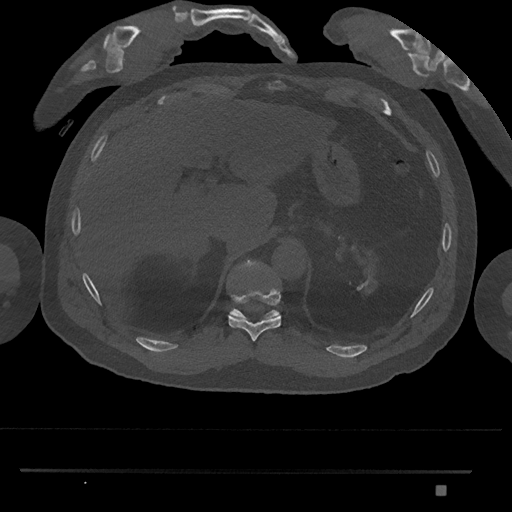
CT including the spine, one axial slice. Position 987 of 1134 along the scan axis. 120 kVp. Bone window (W 1800 / L 400 HU). 512 × 512 image matrix, field of view 429 × 429 mm. Male patient, age 65 years. Case-level facts recorded for this patient, not image findings: primary cancer: prostate.
Outlined on this slice (semi-automatic segmentation, software-assisted and operator-edited):
- T10 vertebra: bounding box (x1, y1, x2, y2) in pixels: (228, 288, 281, 341)
- T11 vertebra: (229, 260, 280, 319)